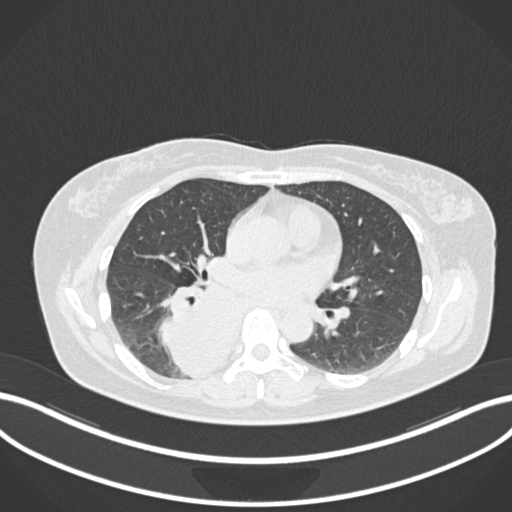
Chest CT, one axial slice. Slice 586 of 677 in the series (ordered by position). Reconstruction kernel B30f. 120 kVp. Lung window (W 1500 / L -600 HU). 1 mm slice thickness. 512 × 512 image matrix, field of view 400 × 400 mm. Female patient, age 54 years. From the clinical record (not read from this slice): clinical TNM (as recorded): T4 N0 M0.
Annotated regions visible in this slice (rectangle marked by the reading radiologist):
- lung tumour (recorded histology: adenocarcinoma): bounding box (x1, y1, x2, y2) in pixels: (154, 271, 242, 379)